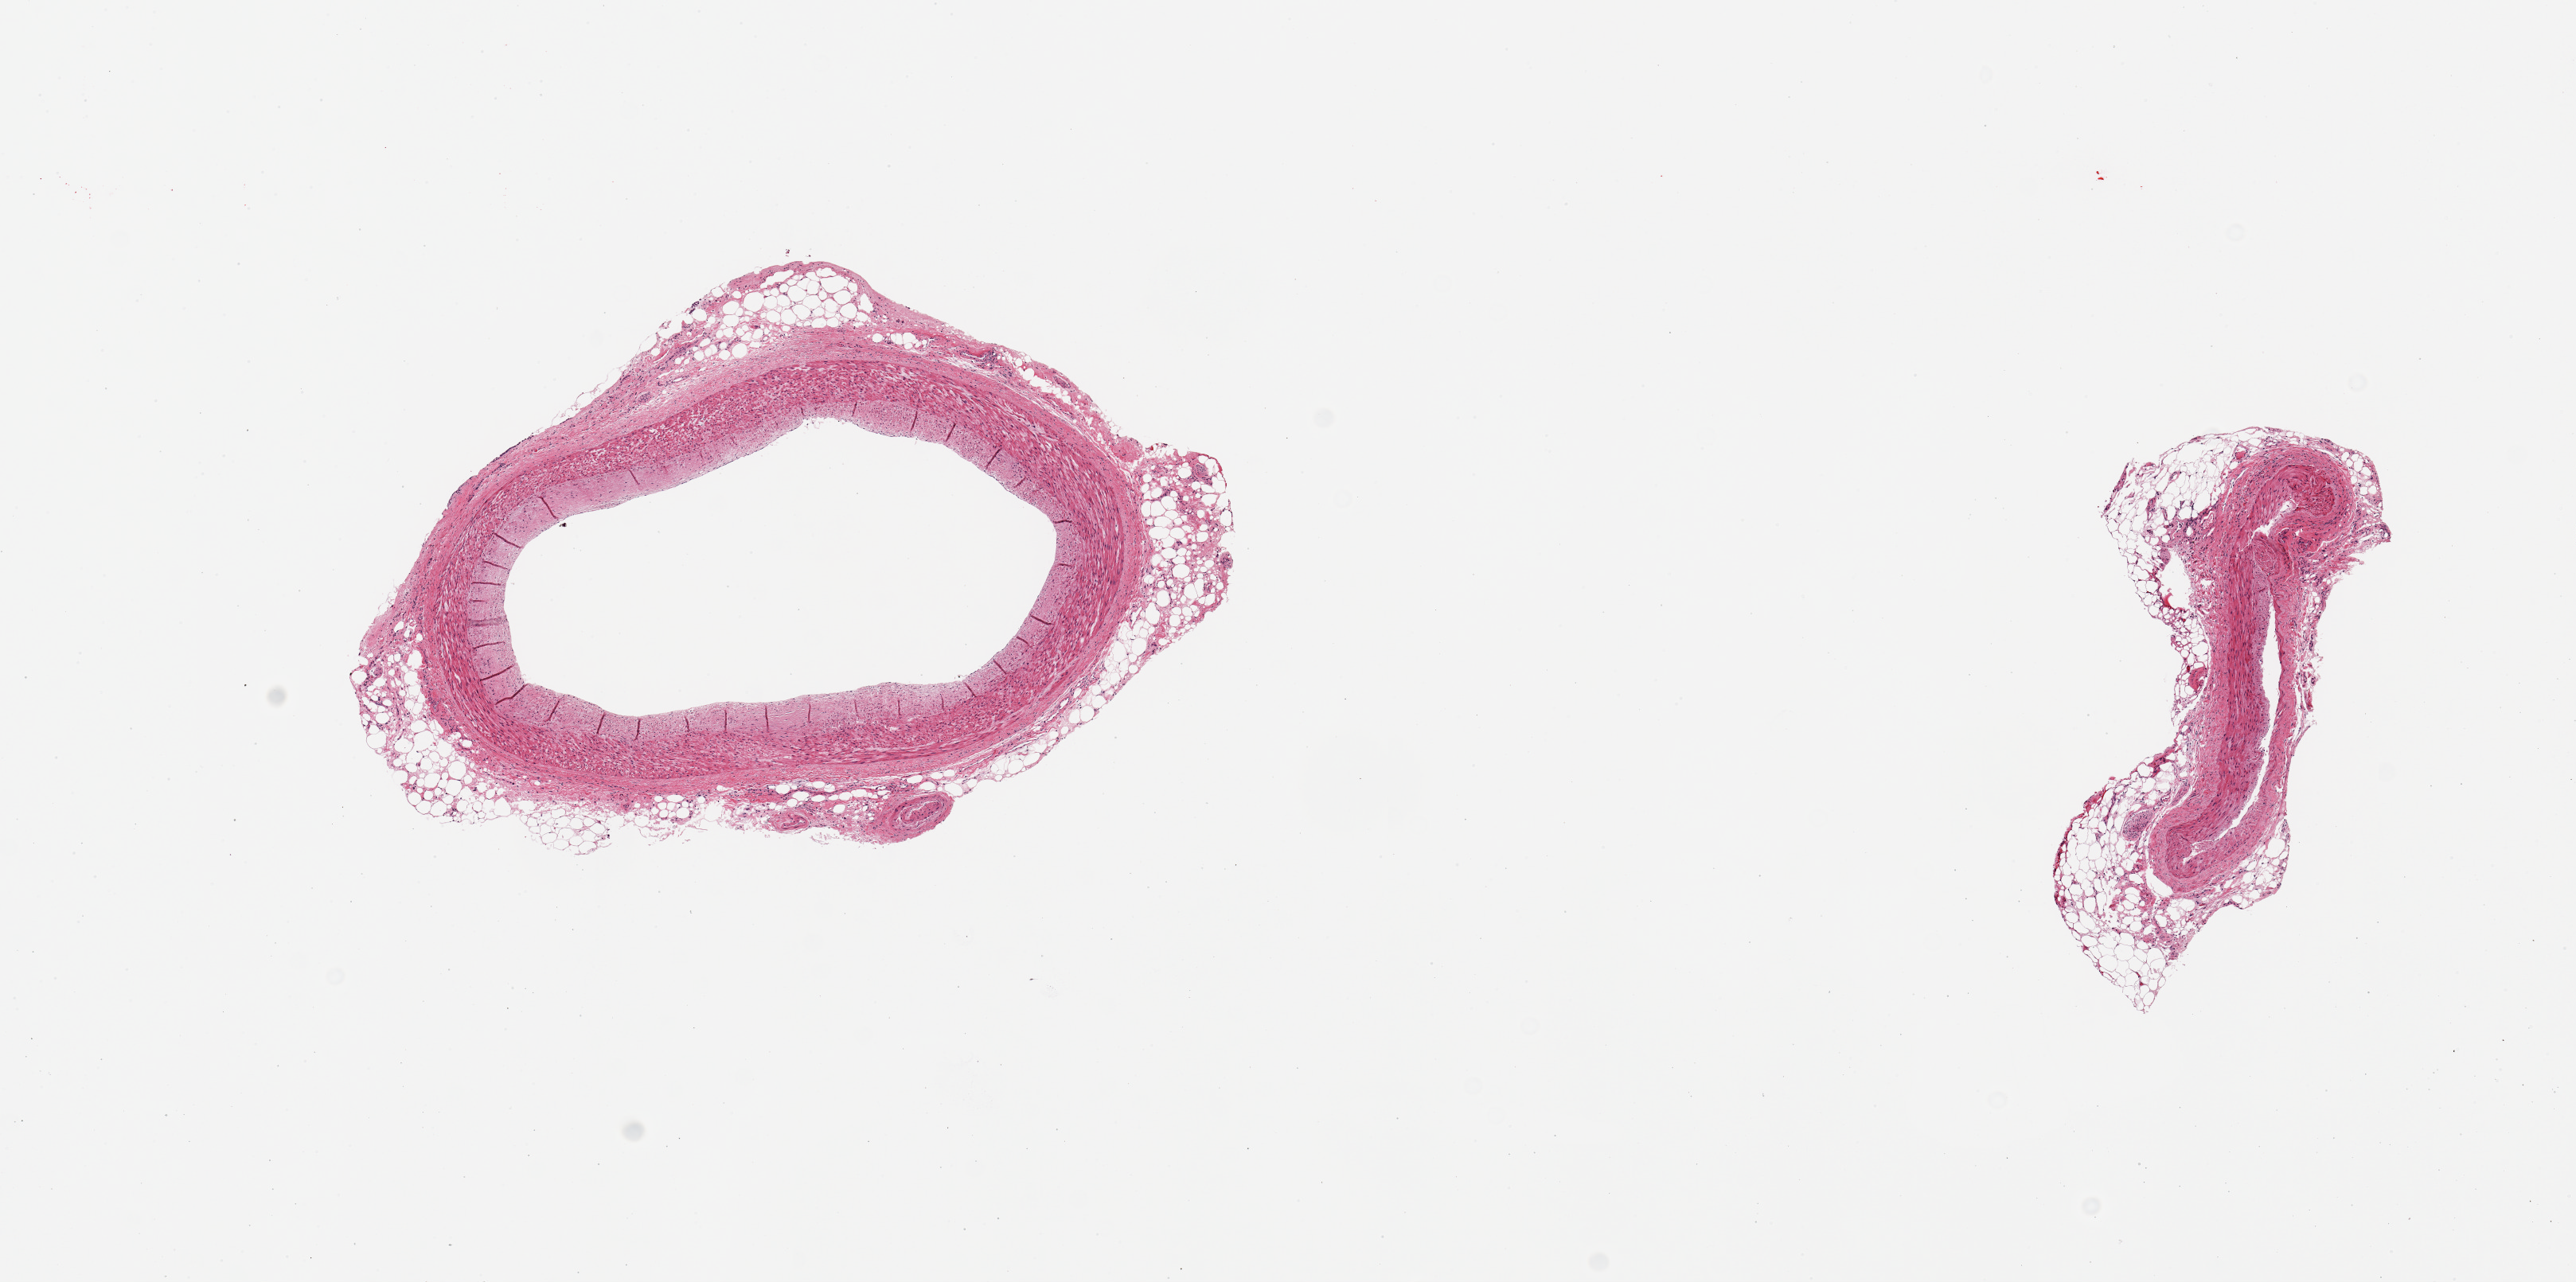
H&E whole-slide image — whole scanned area (about 12.8 x 6.4 mm, acquisition: 20x scan) shown as a low-resolution overview; PAXgene-fixed, paraffin-embedded tissue; target tissue: coronary artery; tissue donor sample.
* pathologist's review note for this sample: 2 pieces, minimal atherosis, ~rim of adherent fat, ~0.5mm